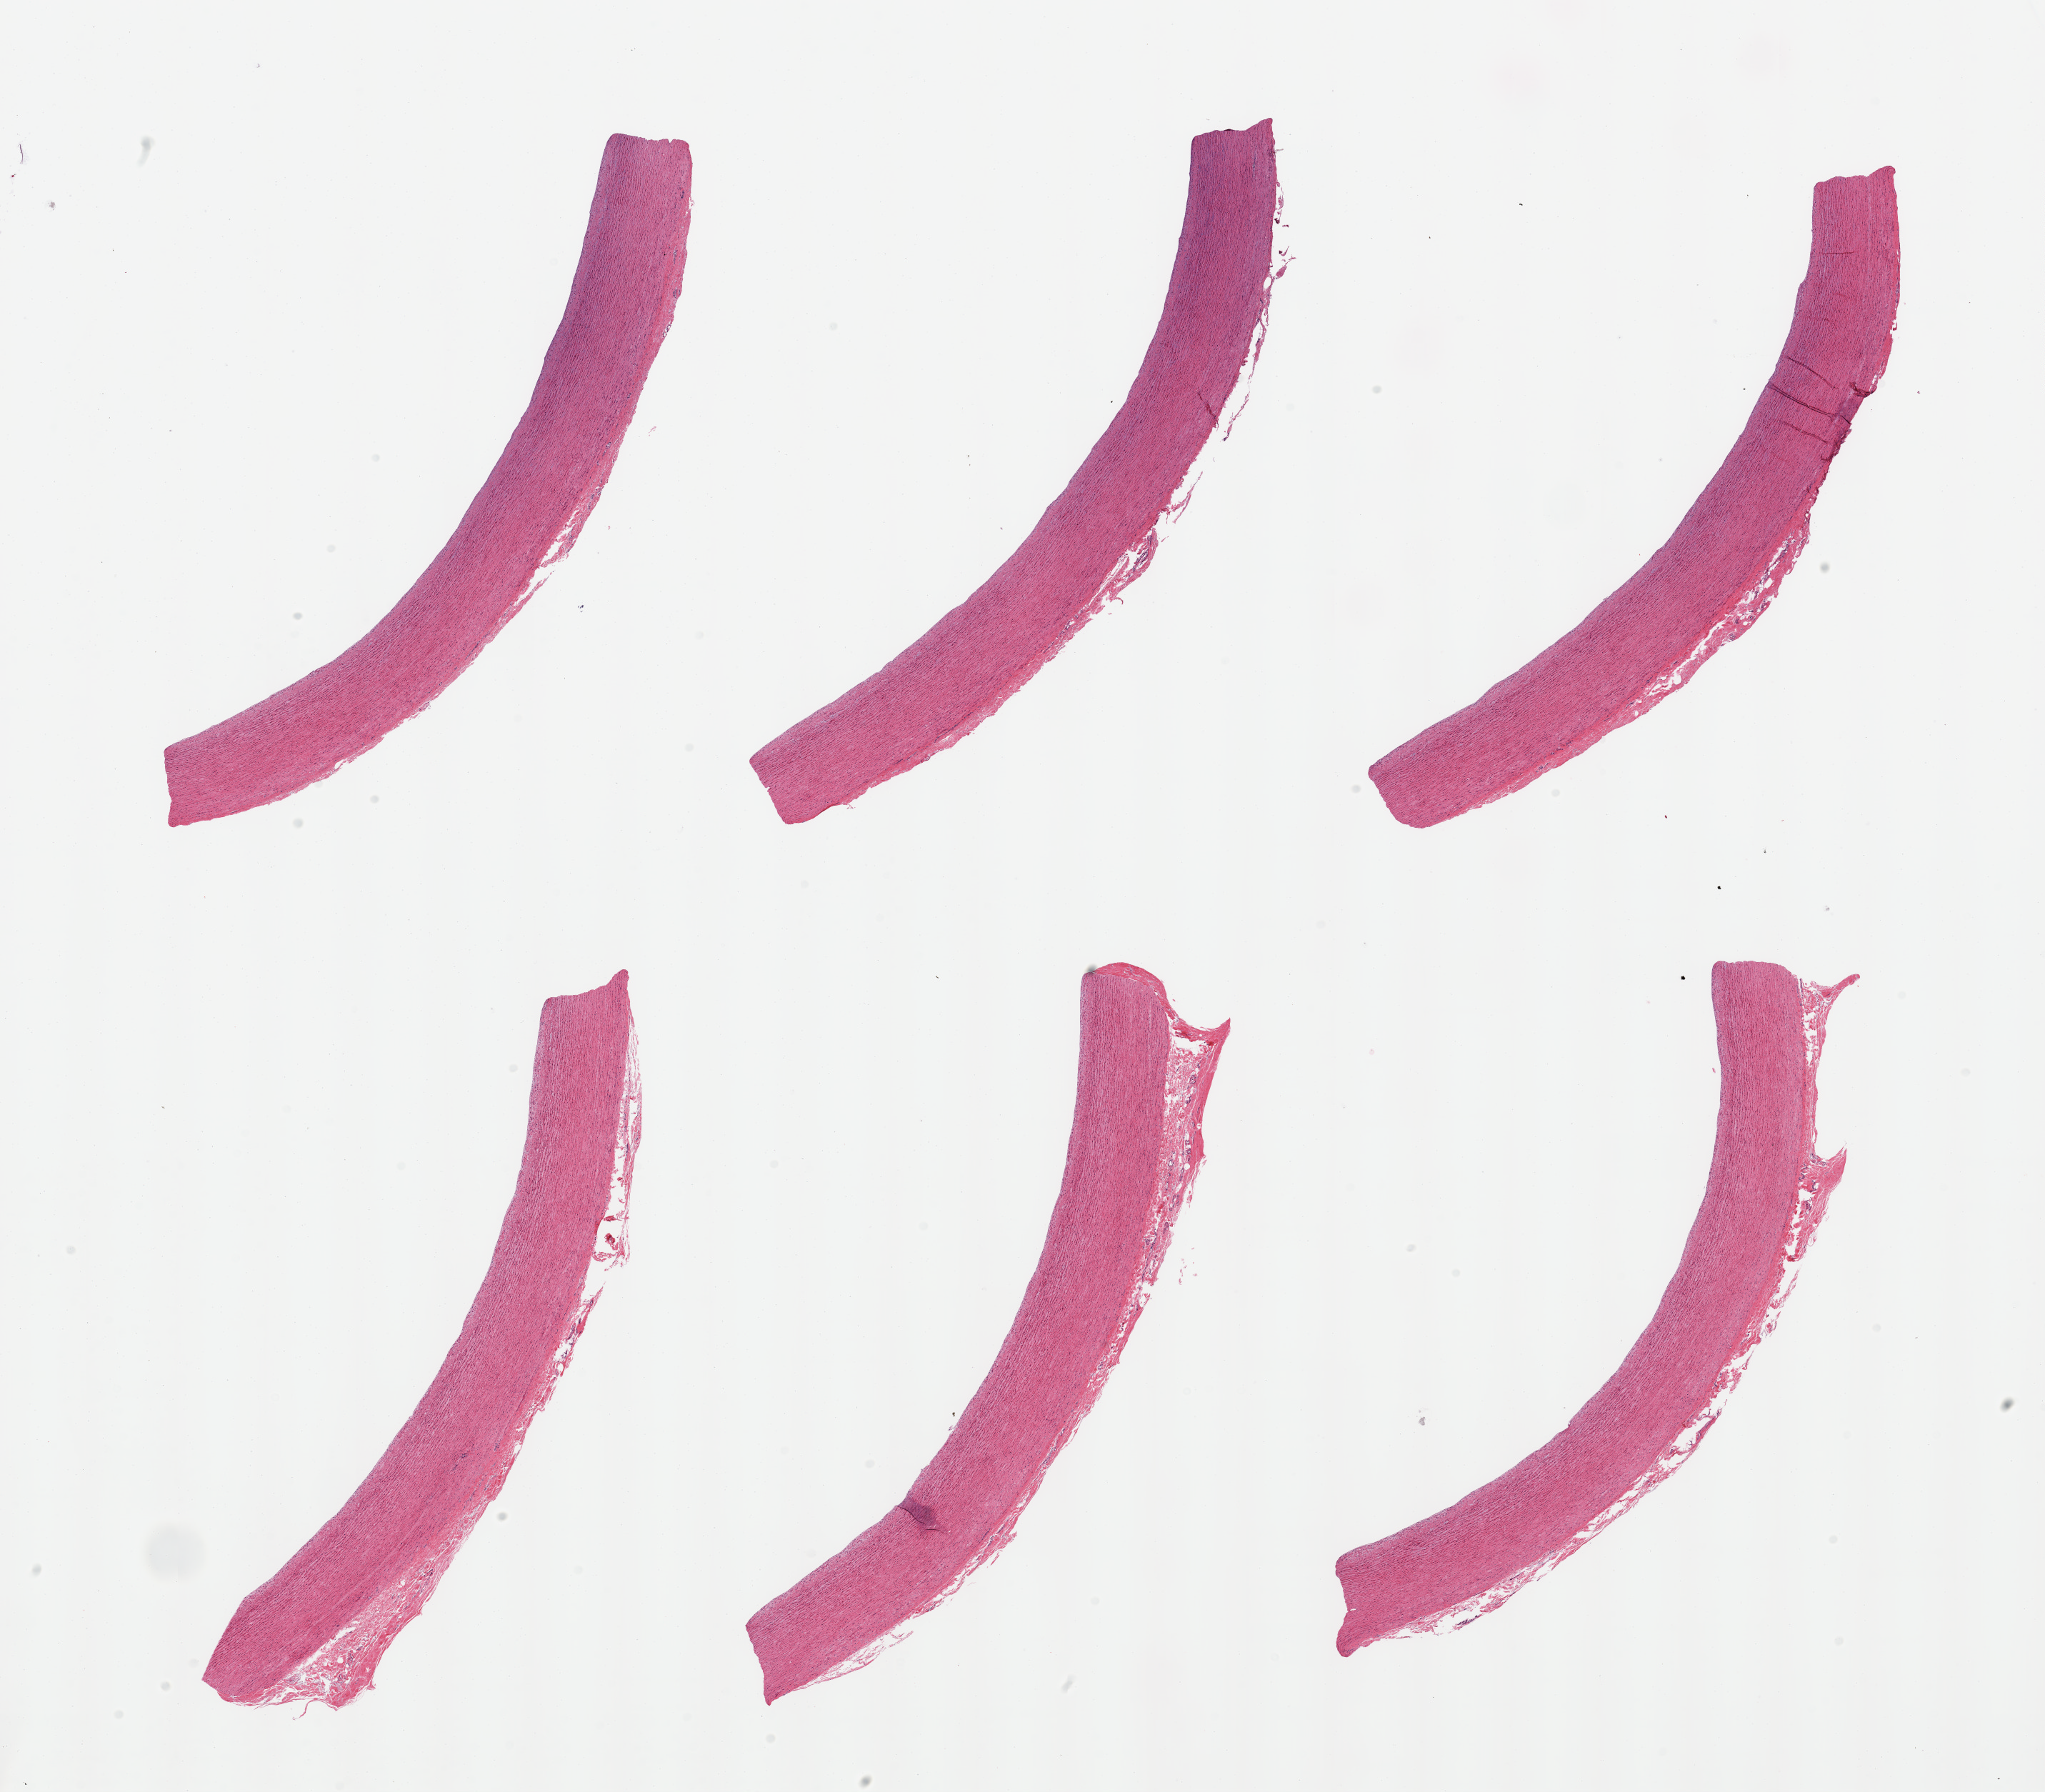
Hematoxylin and eosin (H&E) whole-slide image — low-resolution overview of the scanned area, about 22.6 x 19.8 mm (slide scanned at 20x); PAXgene-fixed paraffin-embedded (PFPE) section; target tissue: aorta; tissue donor sample. Male donor.
Reviewer comment on this tissue sample: 6 pieces, trace atherosis.